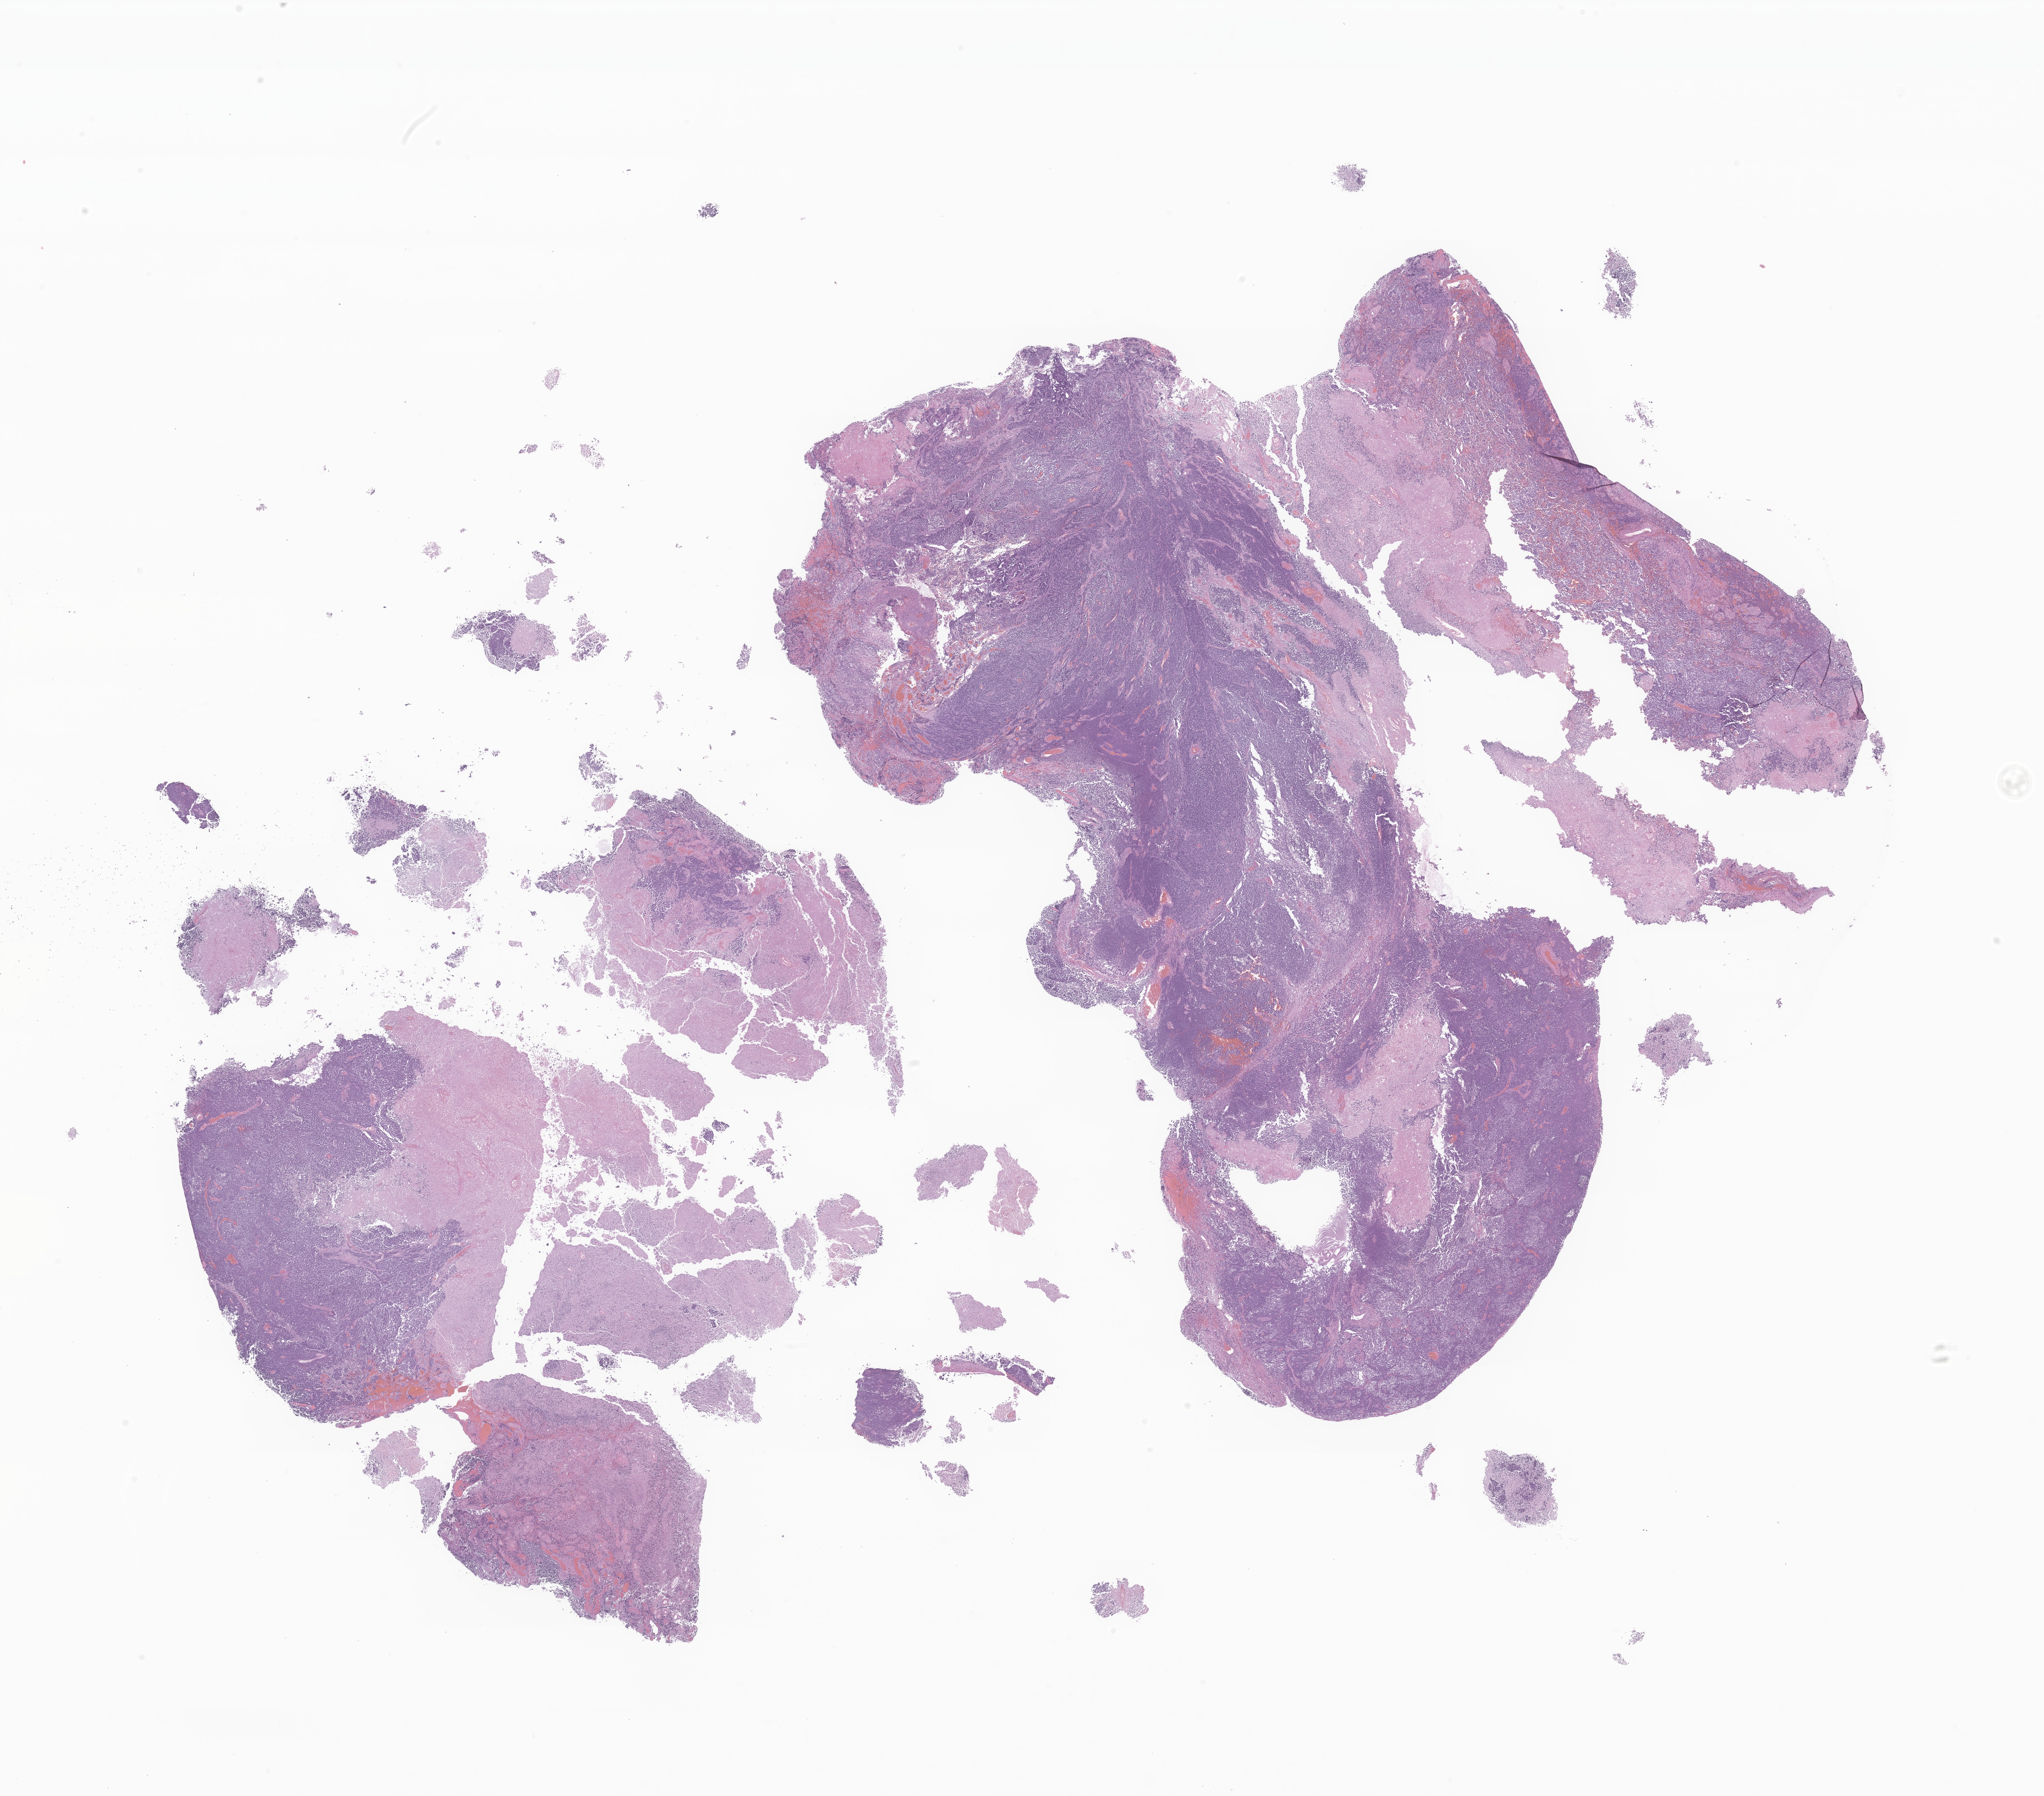
Hematoxylin and eosin (H&E) whole-slide image of tumor tissue from the brain — a low-resolution overview of the entire scanned area, about 25.2 x 22.2 mm, formalin-fixed paraffin-embedded section. Patient female; age 70 months (5 years 10 months).
* recorded diagnosis: Medulloblastoma, NOS